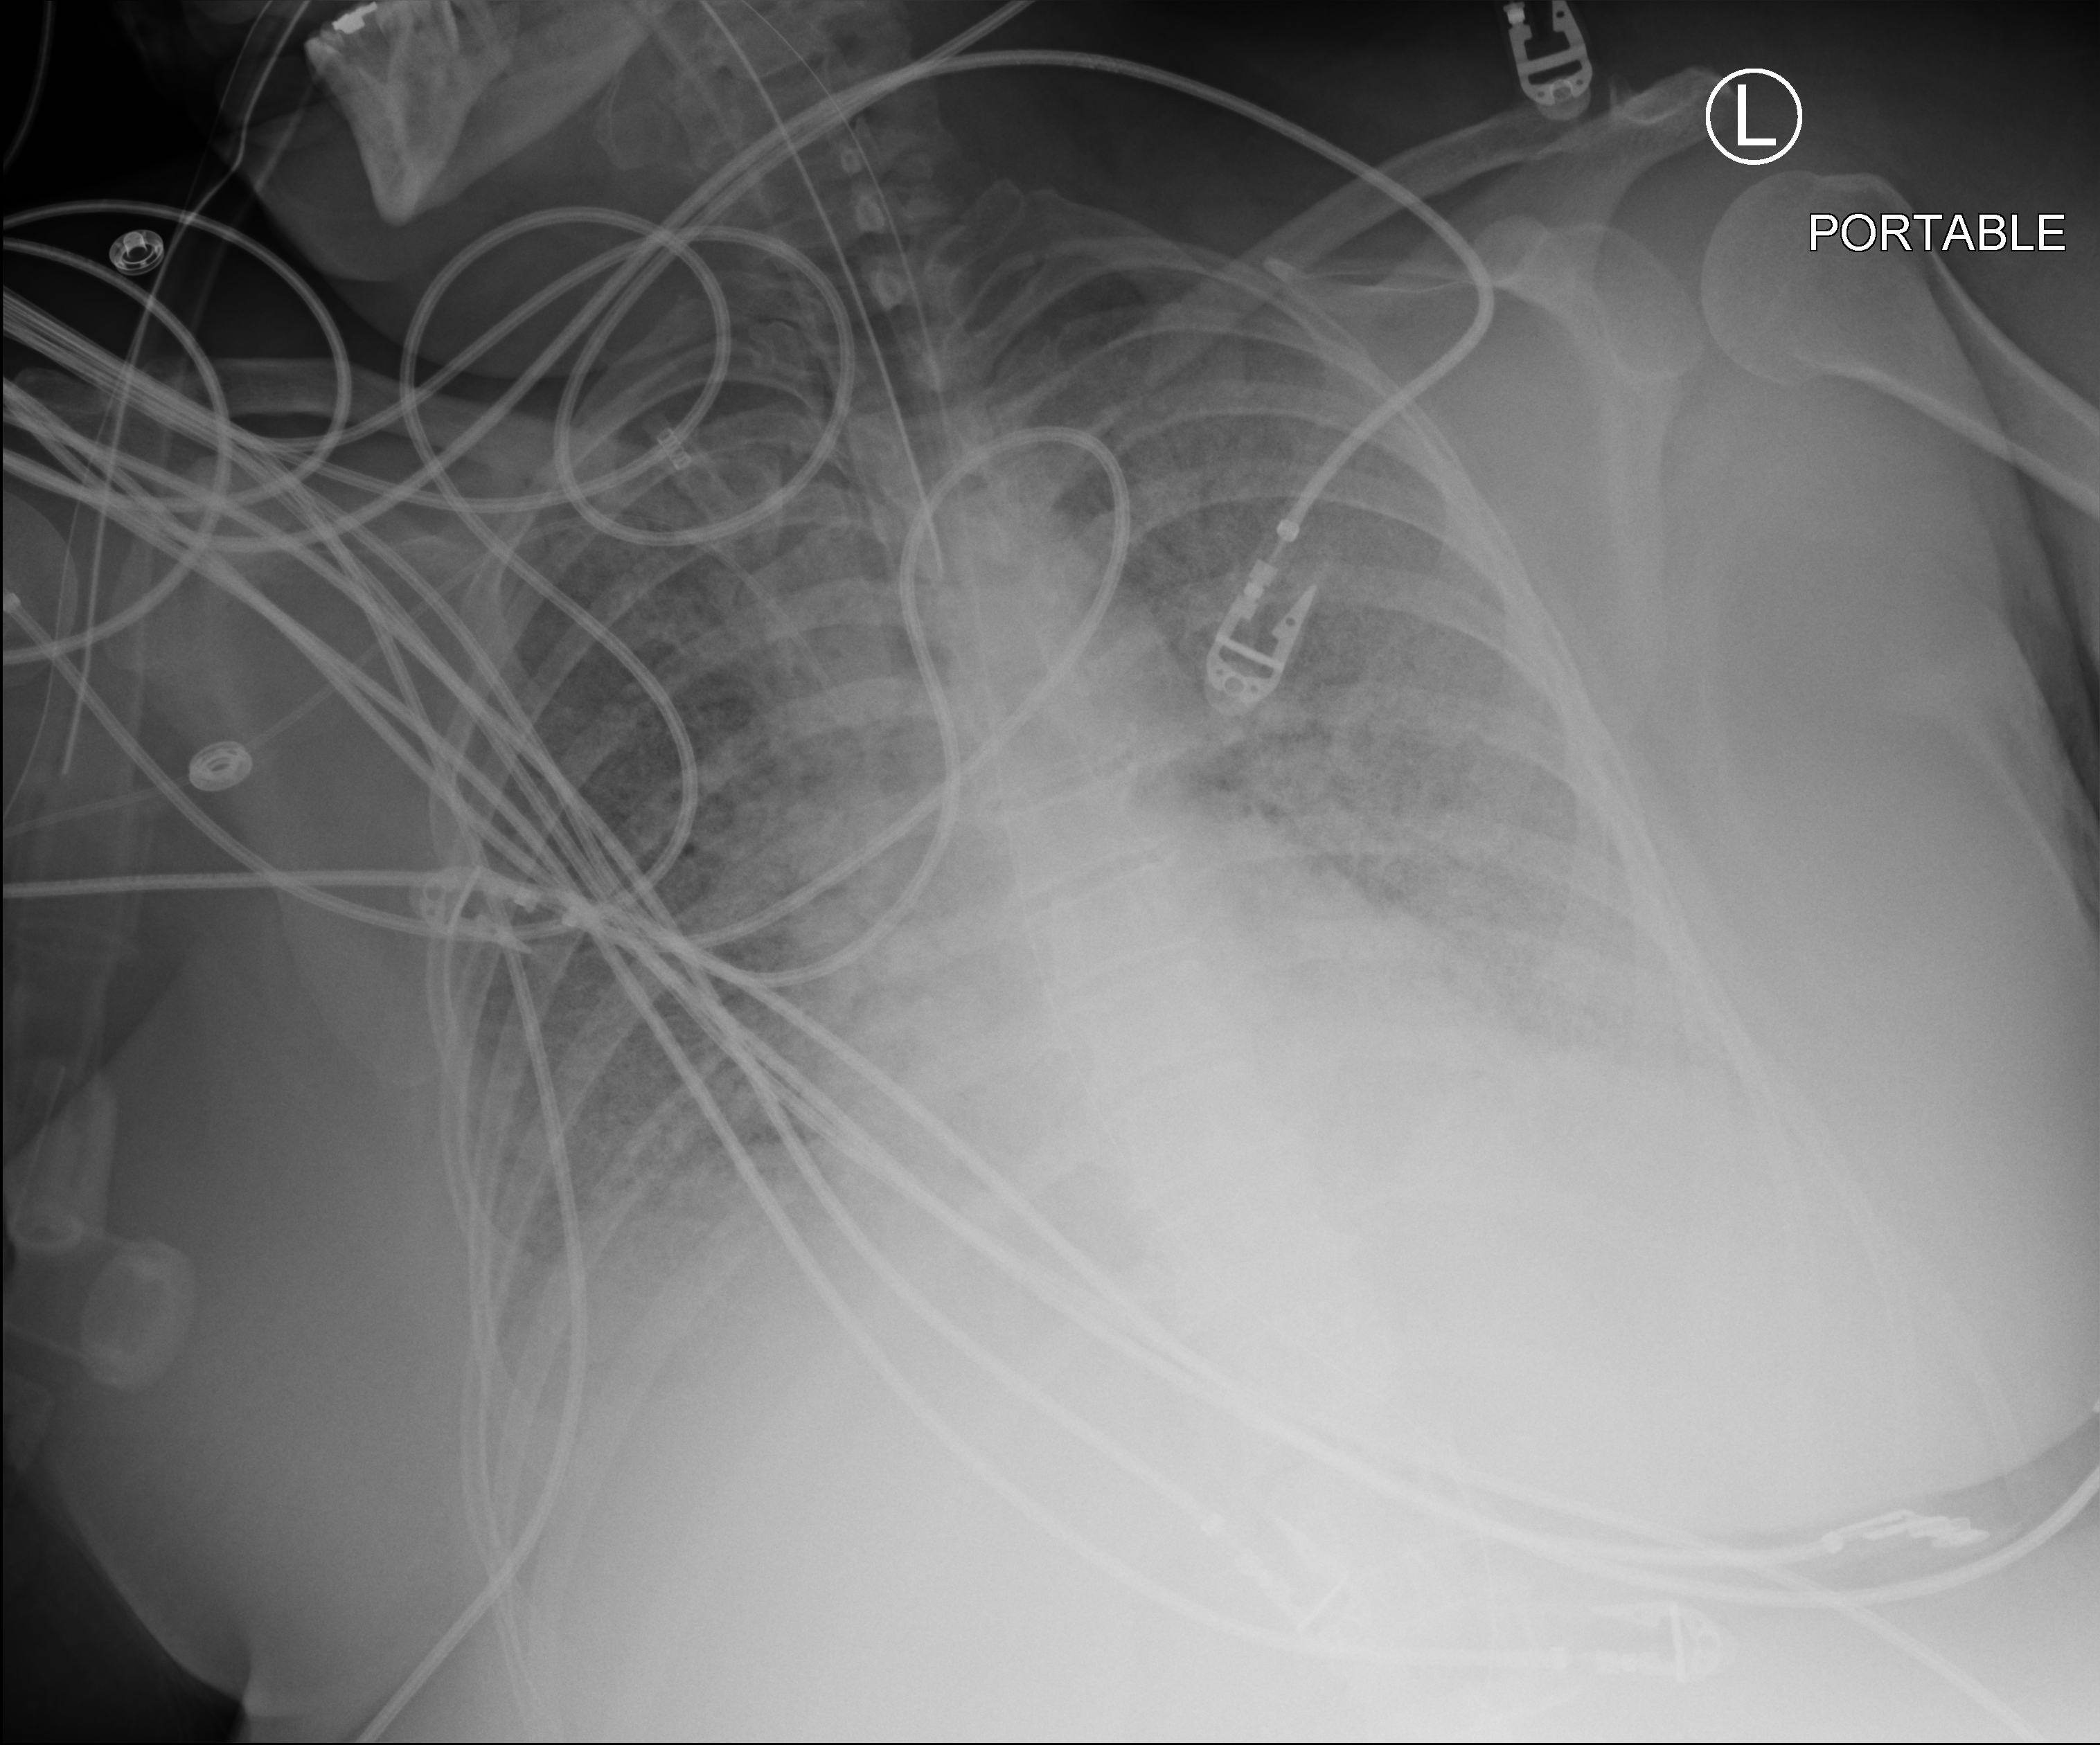
Portable chest radiograph, anteroposterior (AP) projection. Patient hospitalised with COVID-19; female, aged 18–59 years.
Admission-level facts for this patient (not findings on this image; timing relative to this image not recorded):
- mechanically ventilated during this hospital stay: yes
- admitted to intensive care during this hospital stay: yes